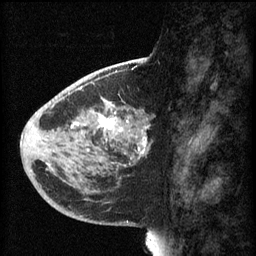
Breast MRI (dynamic contrast-enhanced), one sagittal slice; slice 25 of 60 in the series (ordered by position); 3 images stored at this slice position (order not interpretable as contrast timing); 1.5 T; TE 4.2 ms, TR 8.1 ms; 2 mm slice thickness; 256 × 256 image matrix. Female patient, age 44 years.
Annotated regions visible in this slice (semi-automatically segmented with operator editing):
- analysis volume of interest (the breast-tissue region the enhancement analysis was run in; not a lesion): bounding box [x1, y1, x2, y2] px = [59, 110, 151, 169]
- tumour enhancement mask (voxels above the 70 % enhancement threshold inside the analysis volume of interest): [70, 112, 150, 167]